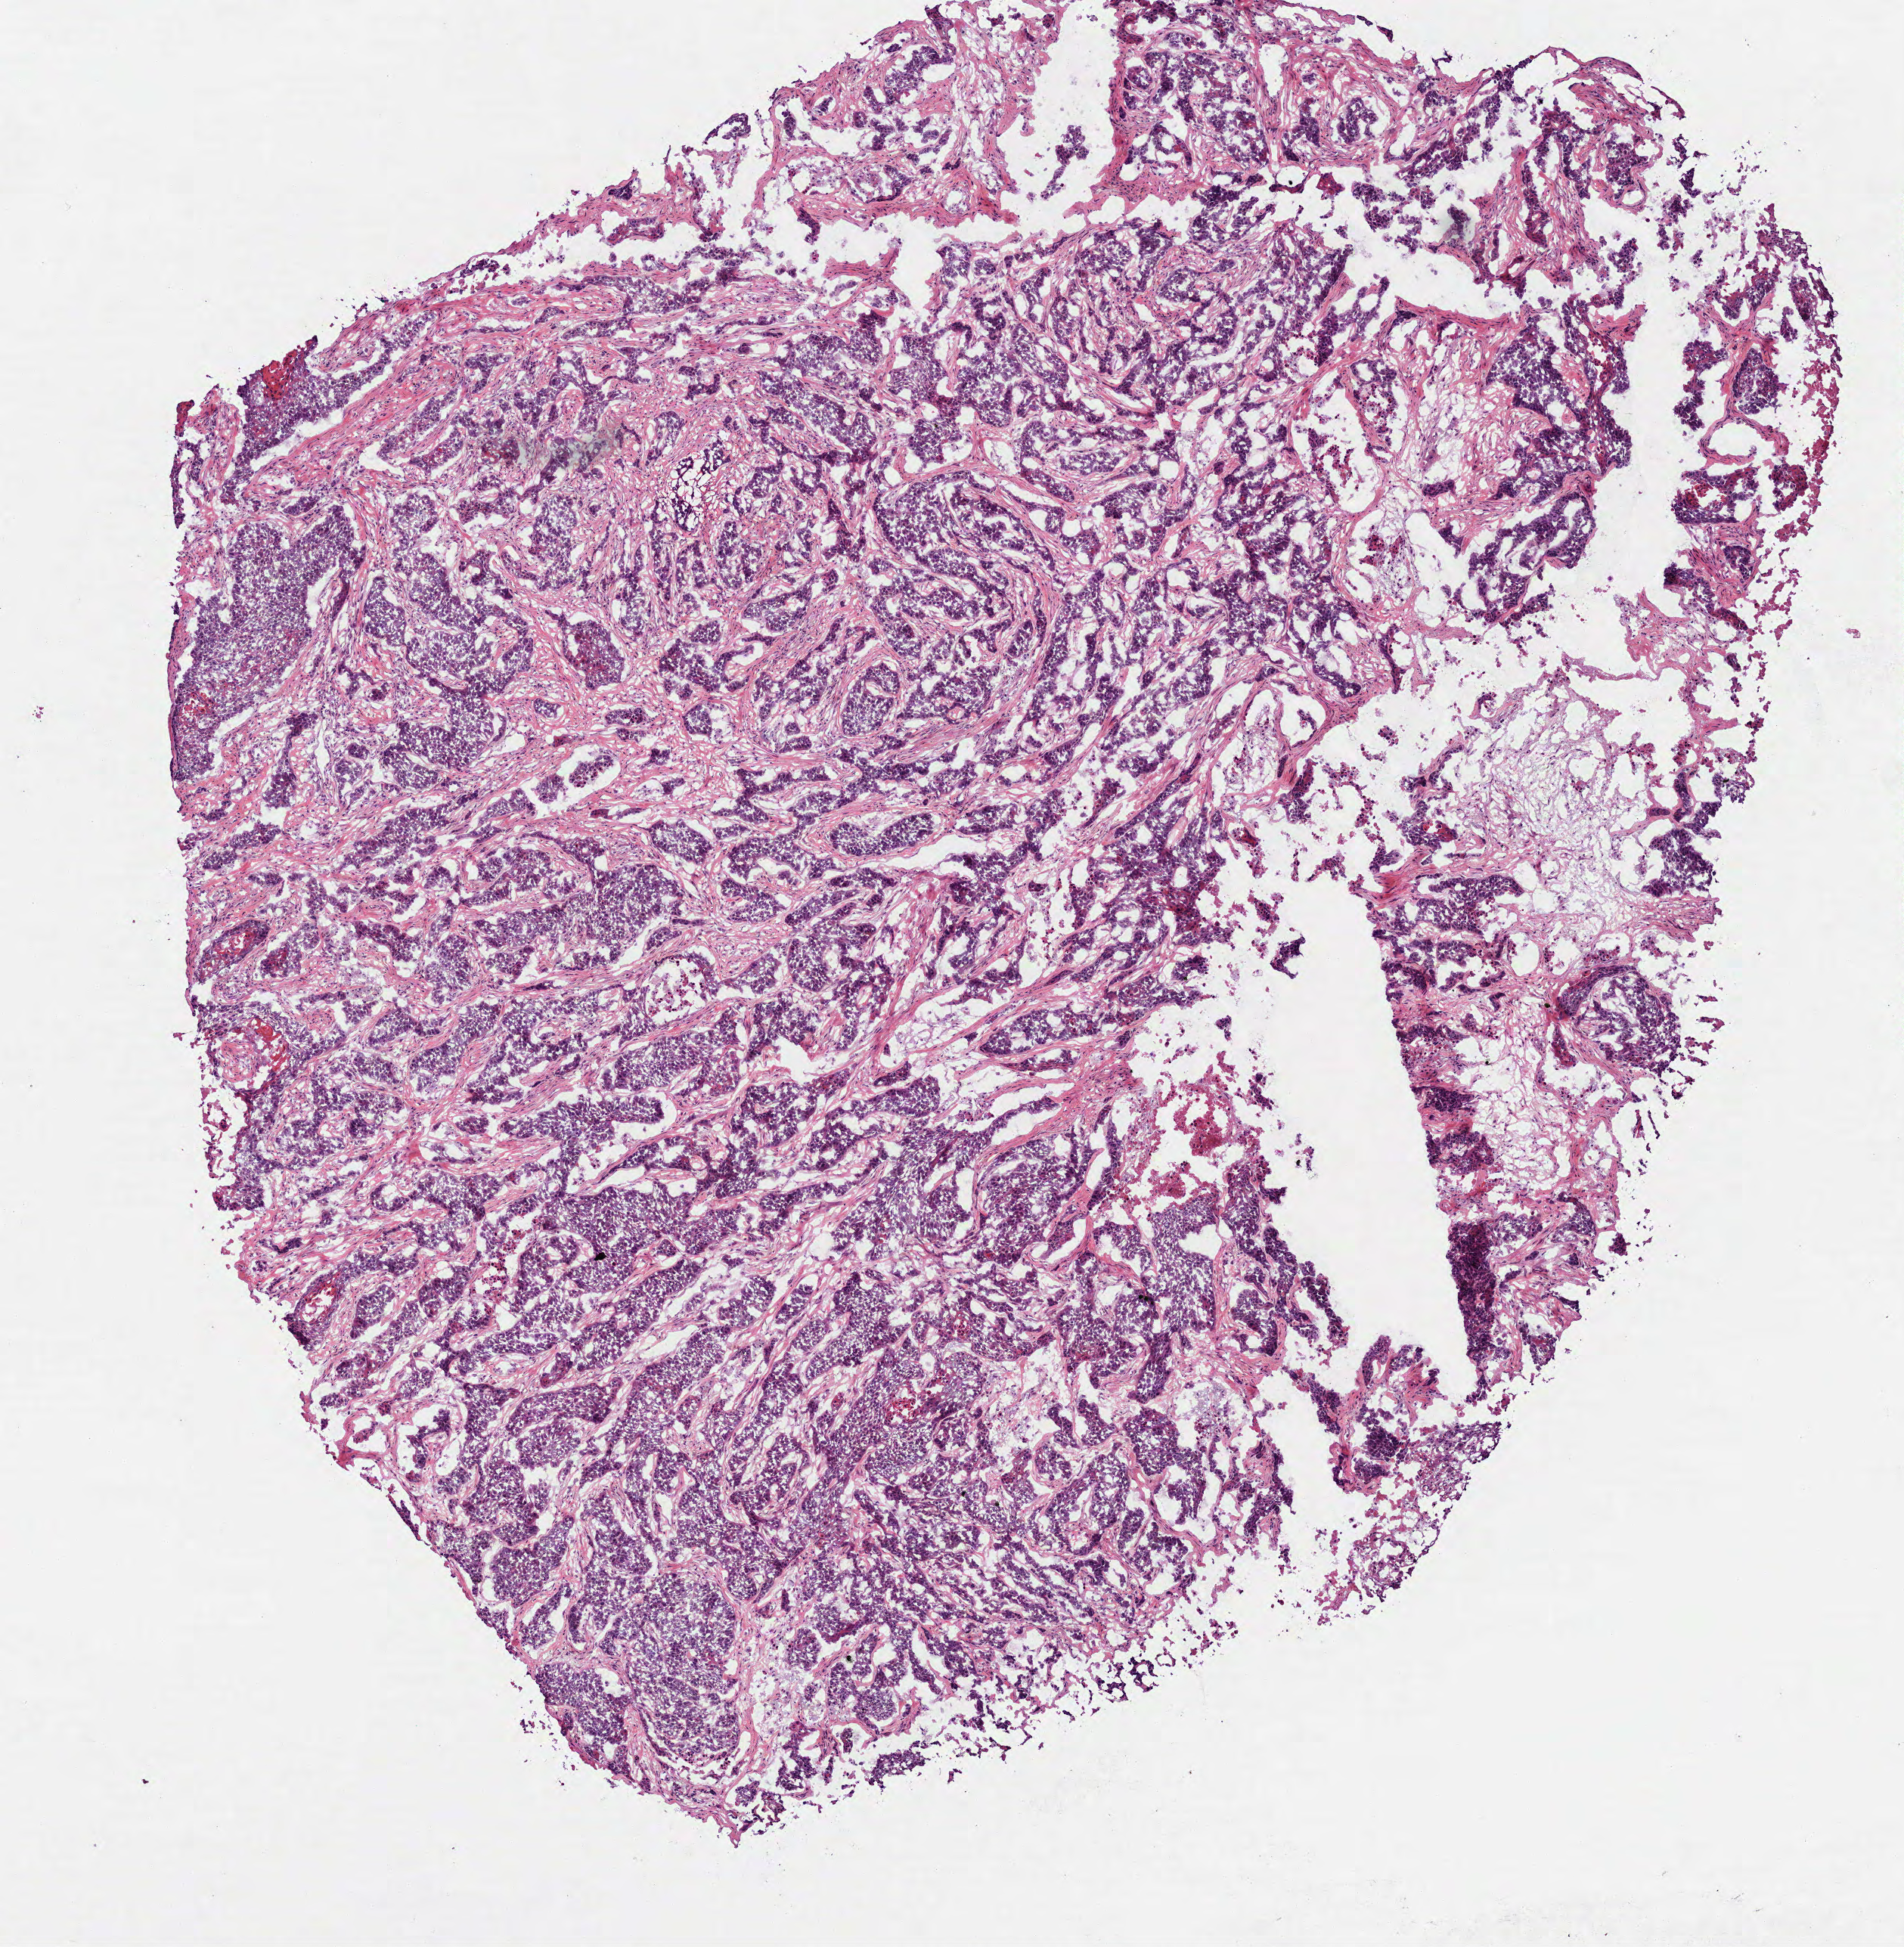
H&E whole-slide image, low-resolution overview of the scanned area, about 5.1 x 5.2 mm (from a 40x scan), frozen section from the top of the tissue portion, head and neck, primary tumour sample. Female patient; age at initial diagnosis 79 years.
Histologic diagnosis: Squamous cell carcinoma, NOS (floor of mouth, NOS).